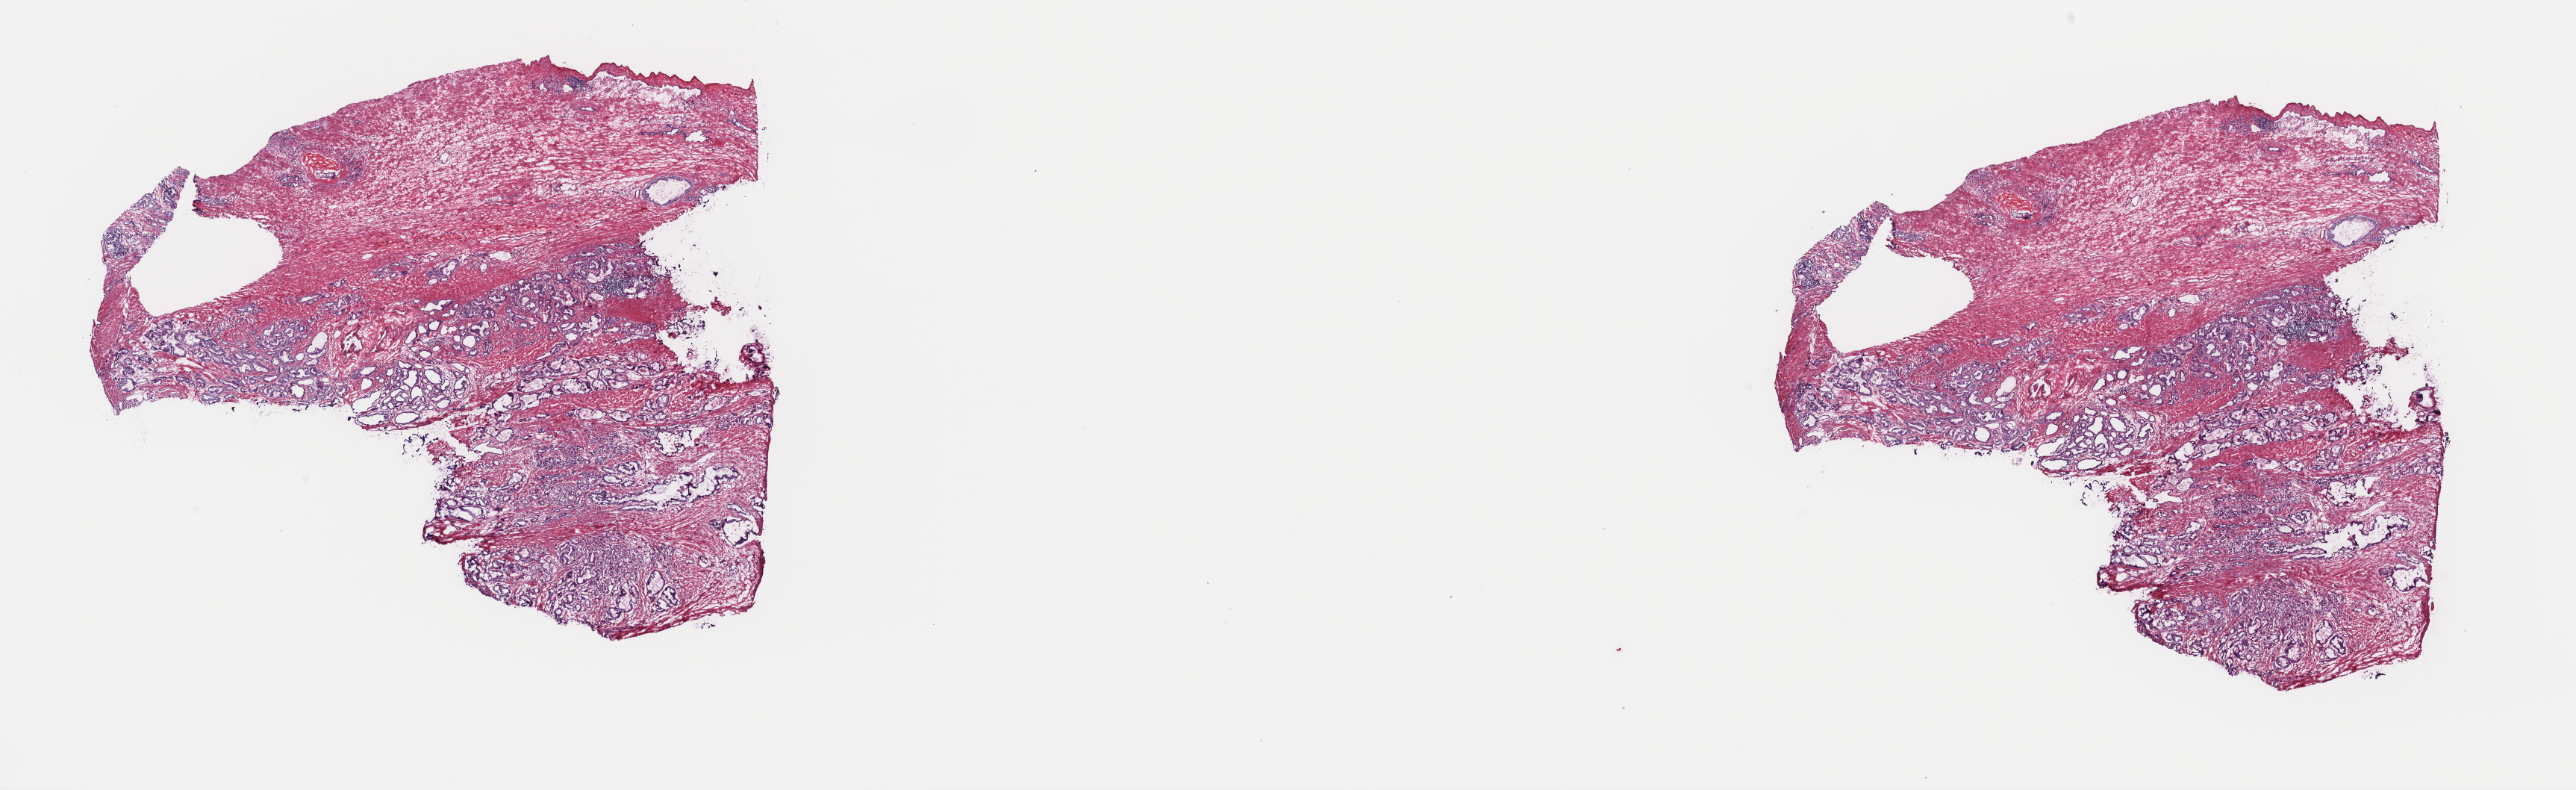
H&E-stained whole-slide image, whole scanned area (about 27.3 x 8.4 mm, acquisition: 40x scan) shown as a low-resolution overview. Frozen section from the top of the tissue portion. Prostate, primary tumour sample. Male, age 64 years at initial diagnosis. Gleason score: 7 (4+3). Pathologist review of this section (percent, as recorded): tumour cells 50%, tumour nuclei 60%, normal cells 40%, stromal cells 10%, necrosis 0%. Inflammatory infiltration, as recorded: lymphocyte infiltration 0%, monocyte infiltration 0%, neutrophil infiltration 0%.
Histologic diagnosis: Adenocarcinoma, NOS (prostate gland). Laterality: bilateral. Lymph nodes positive (case pathology): 0 of 38 examined.